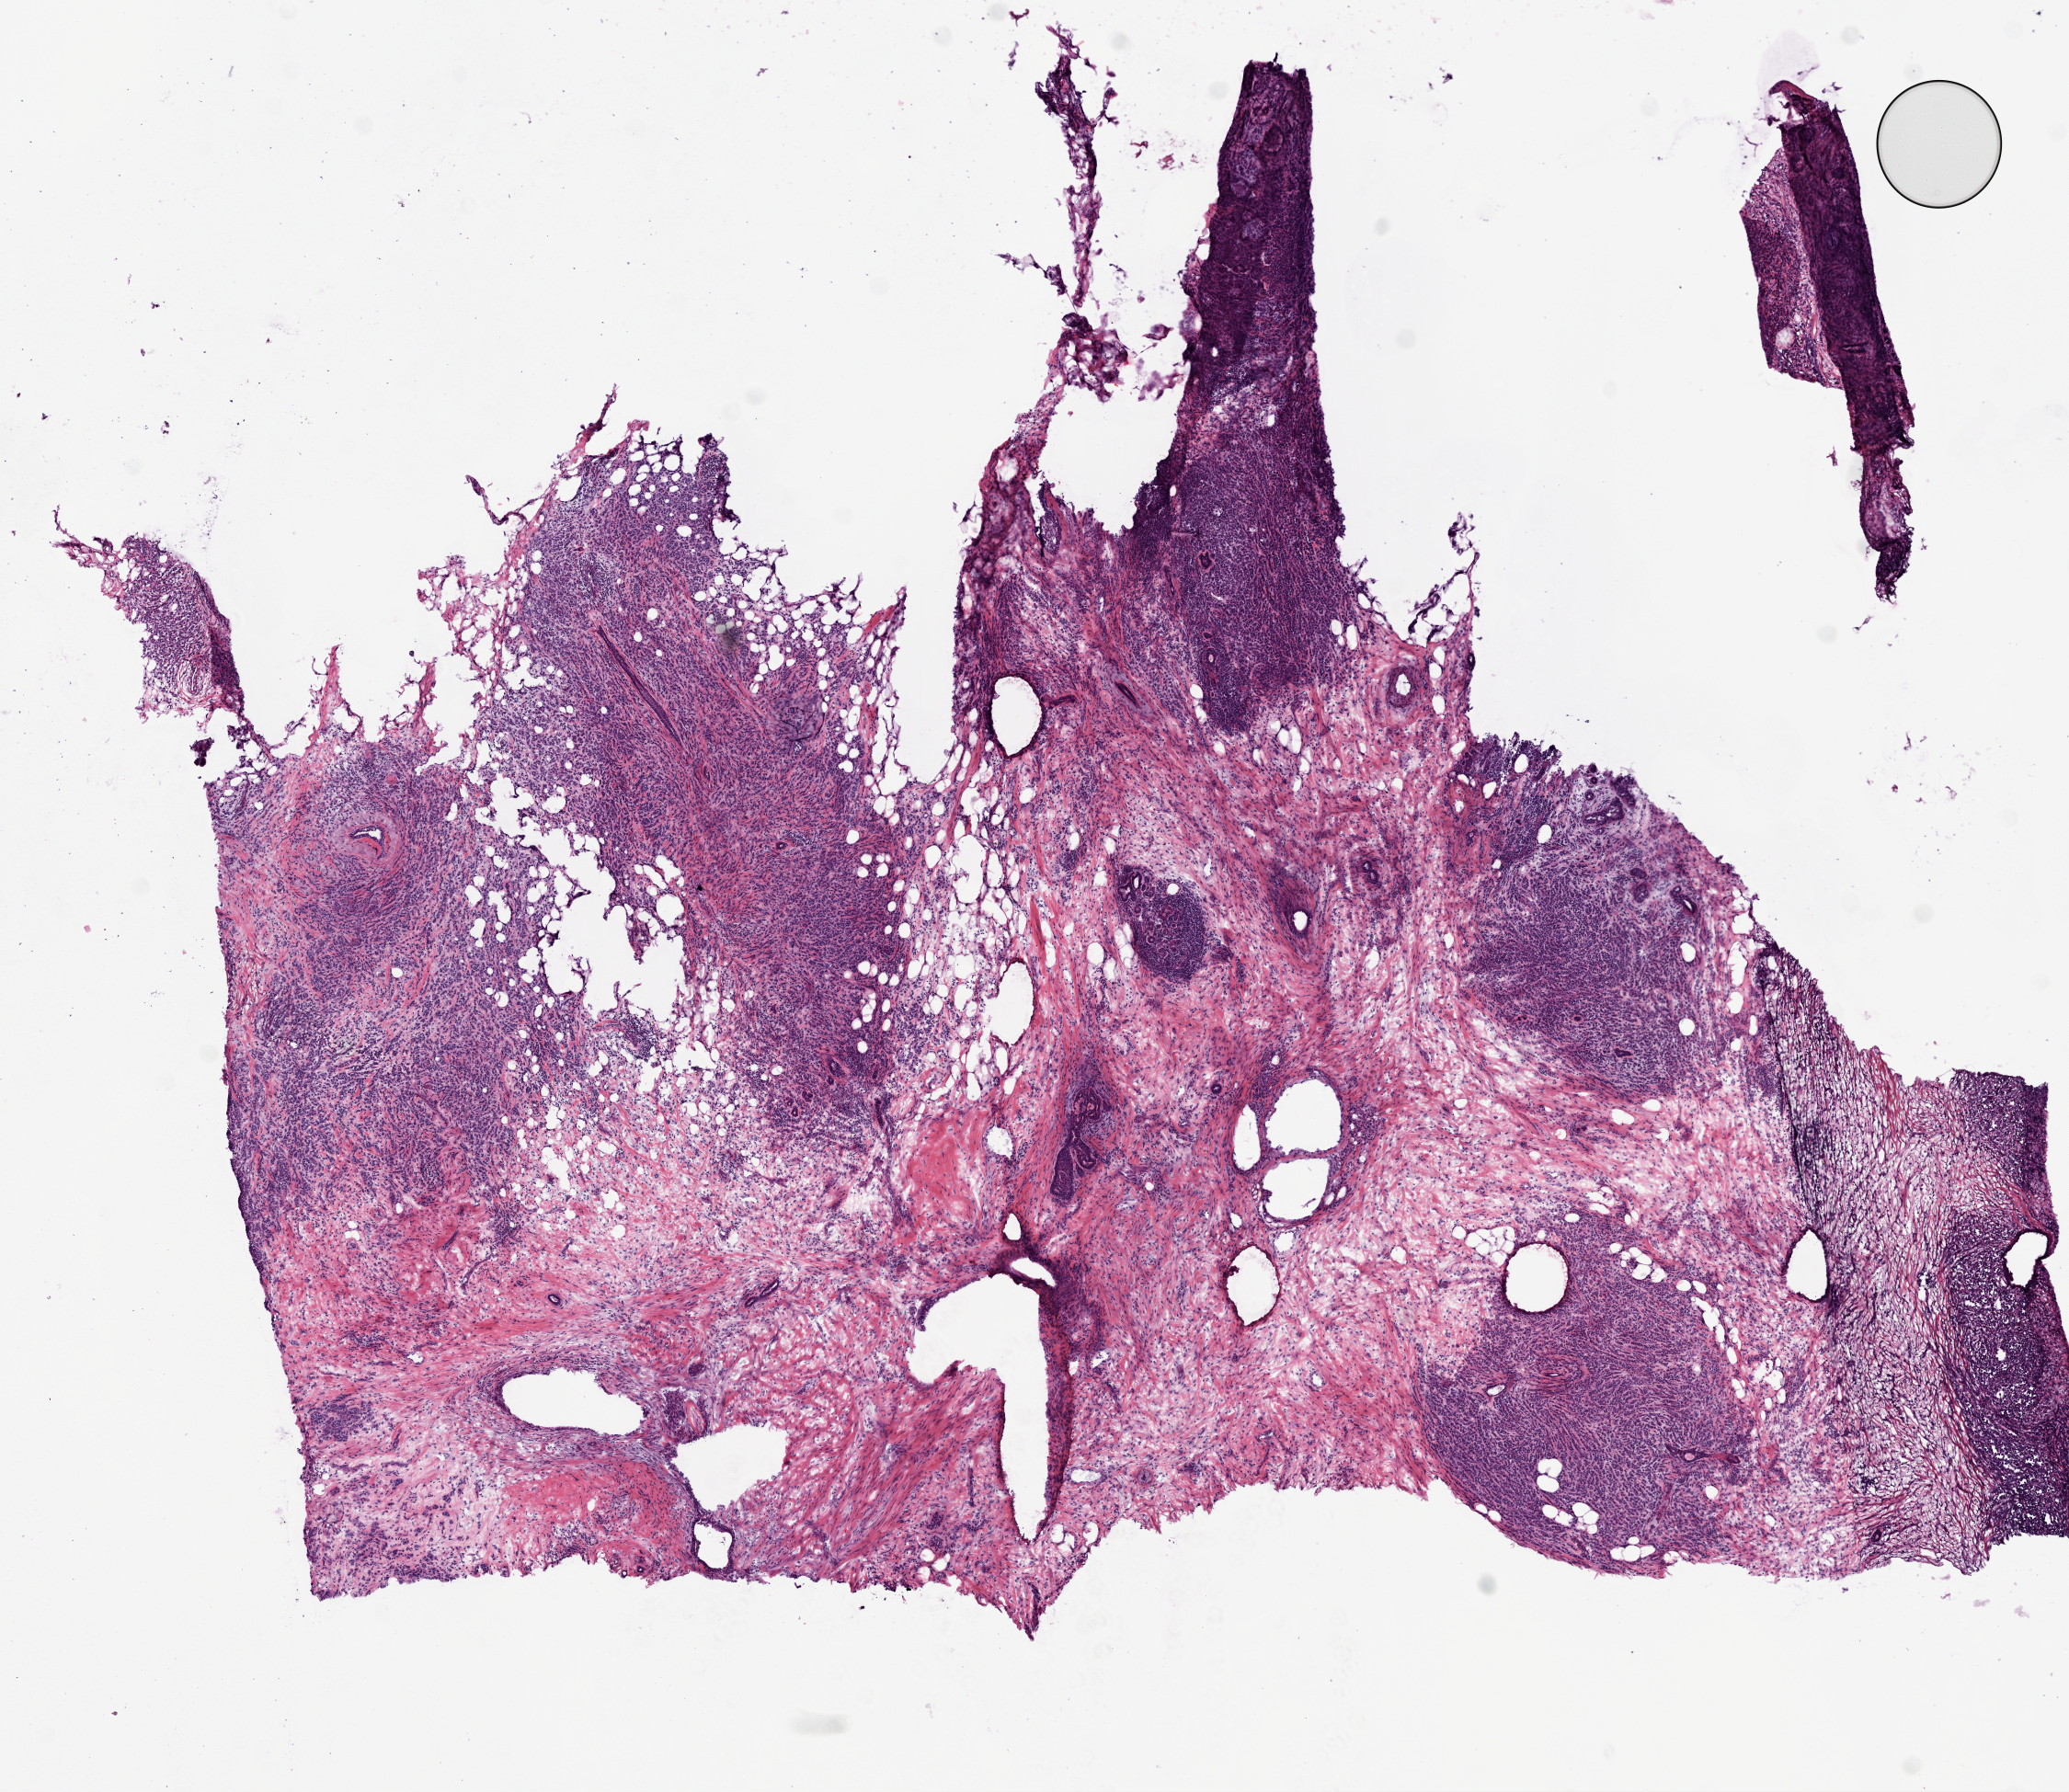
Digitized H&E-stained tissue section (whole slide), shown as a low-resolution overview of the whole scanned area (about 9.0 x 7.8 mm, acquisition: 20x scan). Frozen section from the top of the tissue portion. Breast, primary tumour sample. Female patient; age at initial diagnosis 68 years. Slide review estimates, as recorded: tumour cells 100%, tumour nuclei 80%, normal cells 0%, stromal cells 0%, necrosis 0%. Inflammatory infiltration, as recorded: lymphocyte infiltration 10%, monocyte infiltration 0%, neutrophil infiltration 5%.
- AJCC pathologic stage: IIB (7th edition)
- lymph nodes positive (case pathology): 1 of 3 examined
- pathologic diagnosis: Lobular carcinoma, NOS